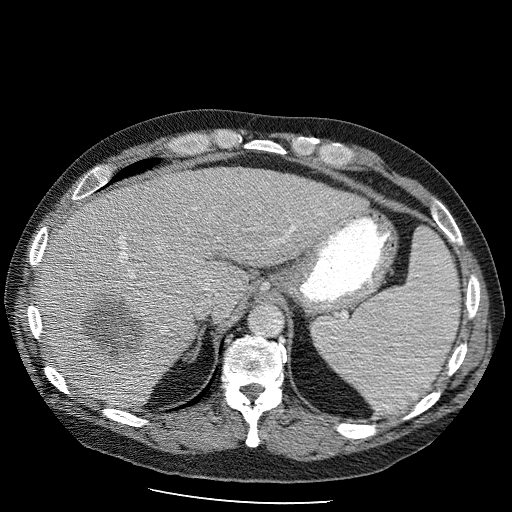
Contrast-enhanced abdominal CT (liver protocol), one axial slice; slice 75 of 98 in the series (ordered by position); reconstruction kernel STANDARD; 120 kVp; soft-tissue window (W 400 / L 40 HU); 2.5 mm slice thickness; 512 × 512 image matrix, field of view 400 × 400 mm. Case-level facts recorded for this patient, not image findings: diagnosis: hepatocellular carcinoma (patient treated with transarterial chemoembolisation; whether this scan precedes or follows treatment is not stated here); TNM stage (as recorded): Stage-II; Child-Pugh class: B; tumour differentiation: moderately differentiated.
Structures marked on this image (semi-automatic segmentation, software-assisted and operator-edited):
- liver parenchyma outside the tumour (the mass and vessels are separate outlines, so this box may not span the whole liver): bounding box [x1, y1, x2, y2] px = [36, 166, 365, 409]
- mass: [77, 291, 149, 360]
- liver vessels: [121, 258, 165, 327]